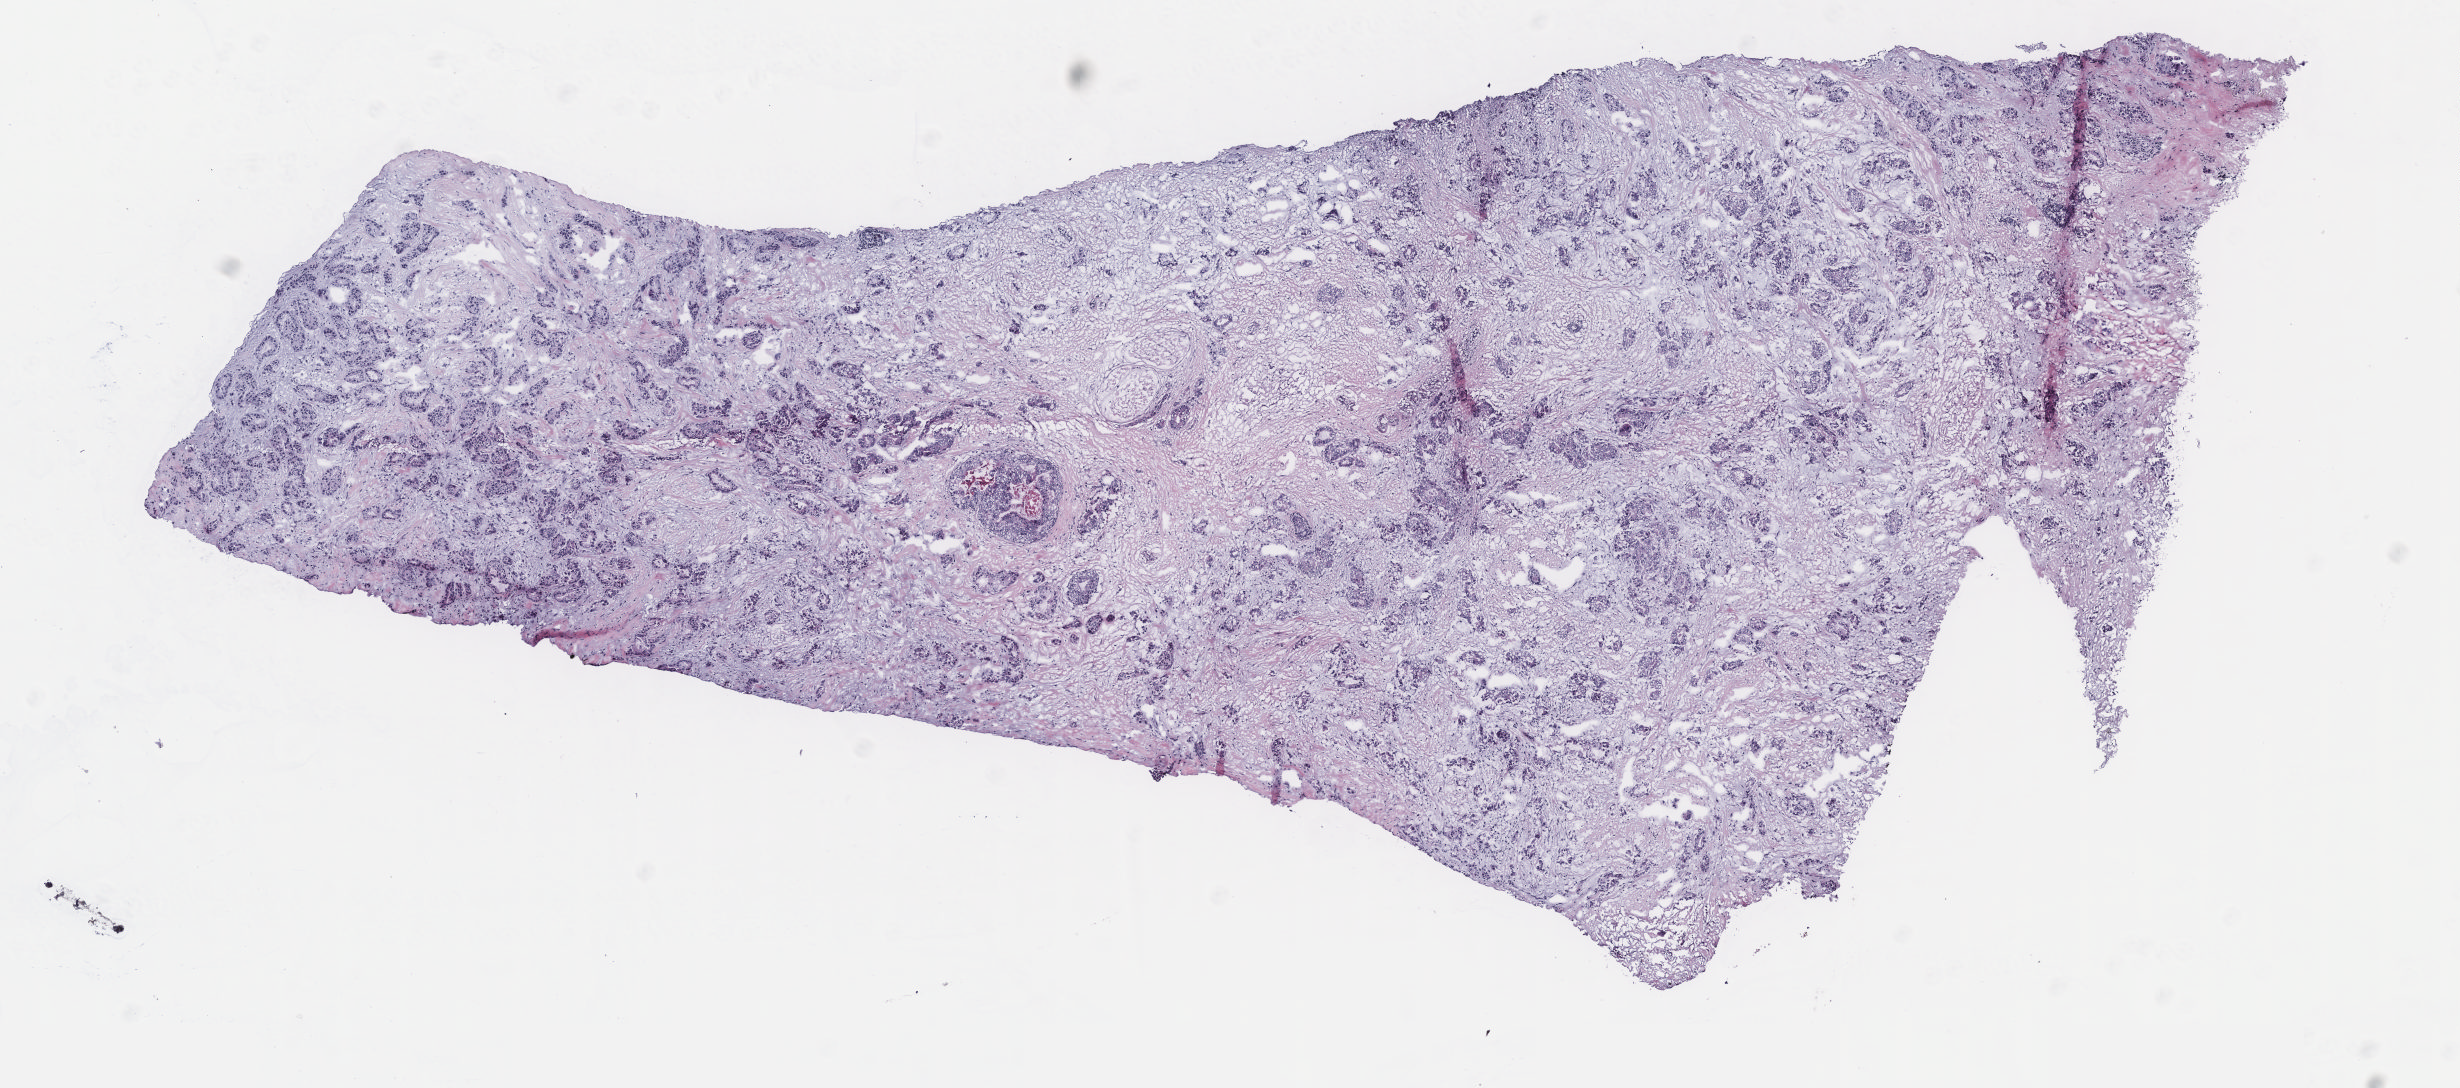
H&E-stained whole-slide image, whole scanned area (about 9.8 x 4.4 mm, acquisition: 40x scan) shown as a low-resolution overview, breast, tumour tissue. 60-year-old female patient.
Histologic diagnosis: Infiltrating duct carcinoma, NOS.